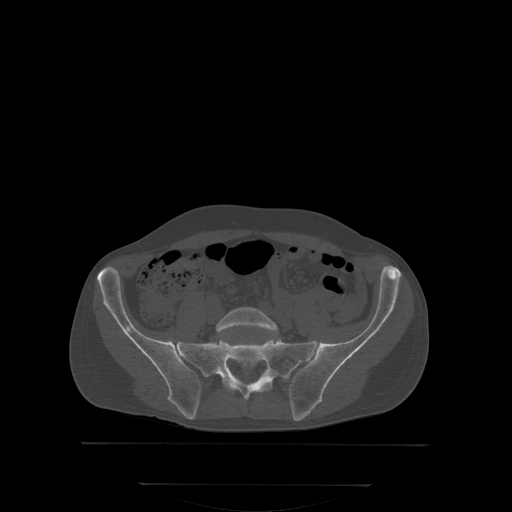
CT including the spine, one axial slice; slice 86 of 350 in the series (ordered by position); bone window (W 1800 / L 400 HU); 2.5 mm slice thickness; 512 × 512 image matrix. Patient: male, 58 years. From the clinical record (not read from this slice): primary cancer: prostate.
Annotated regions visible in this slice (semi-automatic segmentation, software-assisted and operator-edited):
- L5 vertebra: bounding box (x1, y1, x2, y2) in pixels: (217, 307, 278, 335)